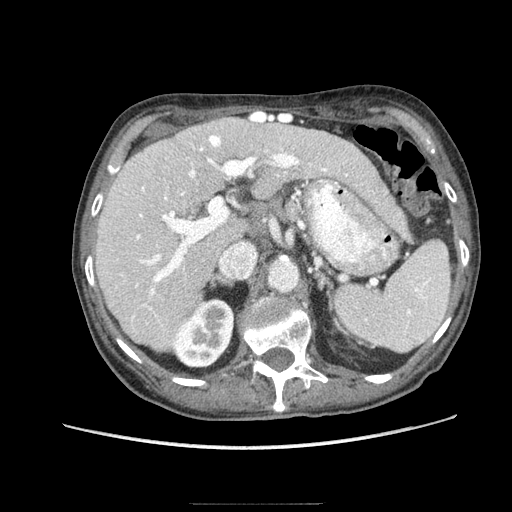
Contrast-enhanced abdominal CT (liver protocol), one axial slice. Position 51 of 83 along the scan axis. Reconstruction kernel STANDARD. 140 kVp. Soft-tissue window (W 400 / L 40 HU). 2.5 mm slice thickness. 512 × 512 image matrix, field of view 360 × 360 mm. Case-level facts recorded for this patient, not image findings: diagnosis: hepatocellular carcinoma (patient treated with transarterial chemoembolisation; whether this scan precedes or follows treatment is not stated here); TNM stage (as recorded): Stage-I; Child-Pugh class: A; tumour differentiation: moderately differentiated; tumour nodularity: uninodular.
Outlined on this slice (semi-automatically segmented with operator editing):
- liver parenchyma outside the tumour (the mass and vessels are separate outlines, so this box may not span the whole liver): bounding box [x1, y1, x2, y2] px = [96, 116, 354, 350]
- liver vessels: [121, 135, 328, 326]